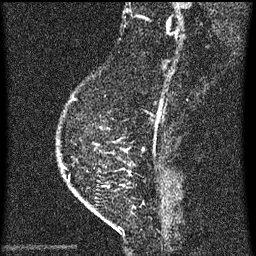
Breast MRI (dynamic contrast-enhanced), one sagittal slice; position 15 of 60 along the scan axis; dynamic contrast-enhanced series, image 2 of 3 at this slice position (ordered by acquisition); 1.5 T; TE 4.2 ms, TR 8 ms; 2 mm slice thickness; 256 × 256 image matrix, field of view 180 × 180 mm. Patient: female, 47 years.
Annotated regions visible in this slice (semi-automatic segmentation, software-assisted and operator-edited):
- analysis volume of interest (the breast-tissue region the enhancement analysis was run in; not a lesion): box from (x=59, y=100) to (x=134, y=203) px
- tumour enhancement mask (voxels above the 70 % enhancement threshold inside the analysis volume of interest): (x=62, y=166)–(x=64, y=169)